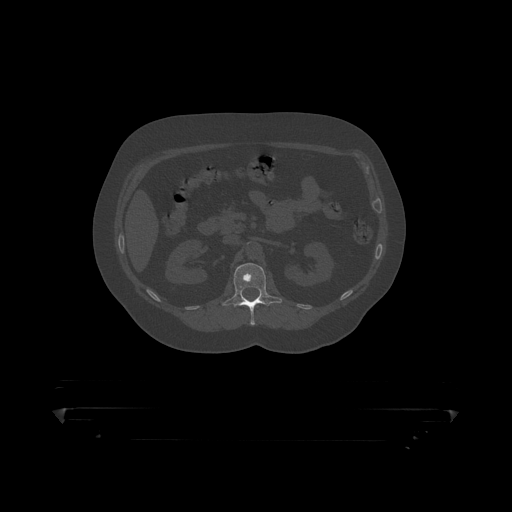
CT including the spine, one axial slice; position 147 of 390 along the scan axis; reconstruction kernel STANDARD; 120 kVp; bone window (W 1800 / L 400 HU); 1.25 mm slice thickness; 512 × 512 image matrix, field of view 650 × 650 mm. Patient: male, 60 years. From the clinical record (not read from this slice): primary cancer: prostate.
Annotated regions visible in this slice (semi-automatic segmentation, software-assisted and operator-edited):
- L1 vertebra: bounding box (x1, y1, x2, y2) in pixels: (222, 263, 283, 319)